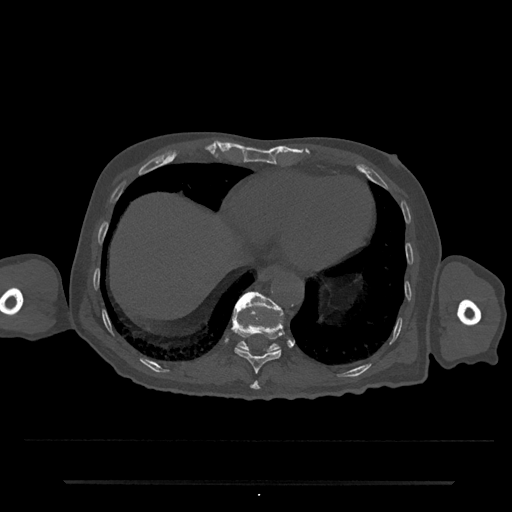
CT including the spine, one axial slice. Slice 297 of 797 in the series (ordered by position). Bone window (W 1800 / L 400 HU). 0.5 mm slice thickness. 512 × 512 image matrix, field of view 427 × 427 mm. Male patient, age 74 years. Case-level facts recorded for this patient, not image findings: primary cancer: prostate.
Outlined on this slice (semi-automatic segmentation, software-assisted and operator-edited):
- T10 vertebra: bounding box <232,315,285,374> (left, top, right, bottom; pixels)
- T11 vertebra: <233,292,283,353>
- T9 vertebra: <250,381,260,390>